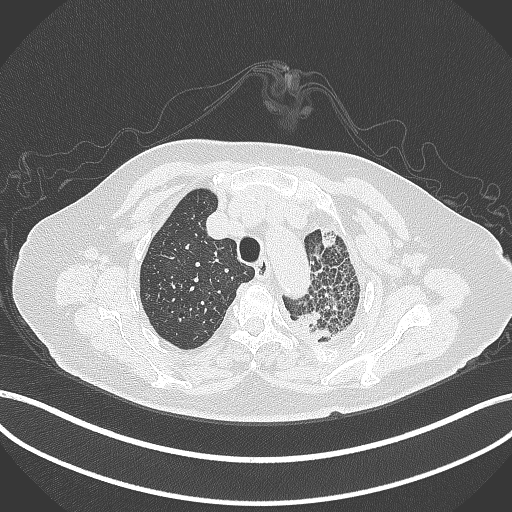
Chest CT, one axial slice; slice 319 of 399 in the series (ordered by position); 120 kVp; lung window (W 1500 / L -600 HU); 1 mm slice thickness; 512 × 512 image matrix, field of view 400 × 400 mm. Patient: female, 75 years. Case-level facts recorded for this patient, not image findings: clinical TNM (as recorded): T3 N3 M1.
Structures marked on this image (bounding box drawn by a radiologist):
- lung tumour (recorded histology: adenocarcinoma): bounding box <292,313,335,346> (left, top, right, bottom; pixels)